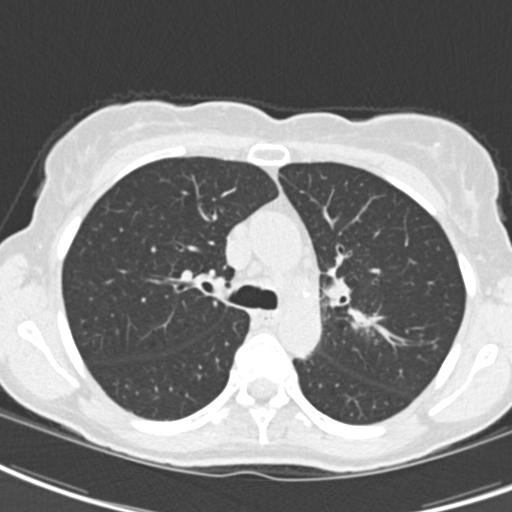
Low-dose screening chest CT, one axial slice; position 135 of 189 along the scan axis; 120 kVp; lung window (W 1500 / L -600 HU); 512 × 512 image matrix.
Annotated regions visible in this slice (manually delineated by an expert):
- lesion 2 (tumor, hilum of left lung): bounding box [x1, y1, x2, y2] px = [328, 282, 350, 301]